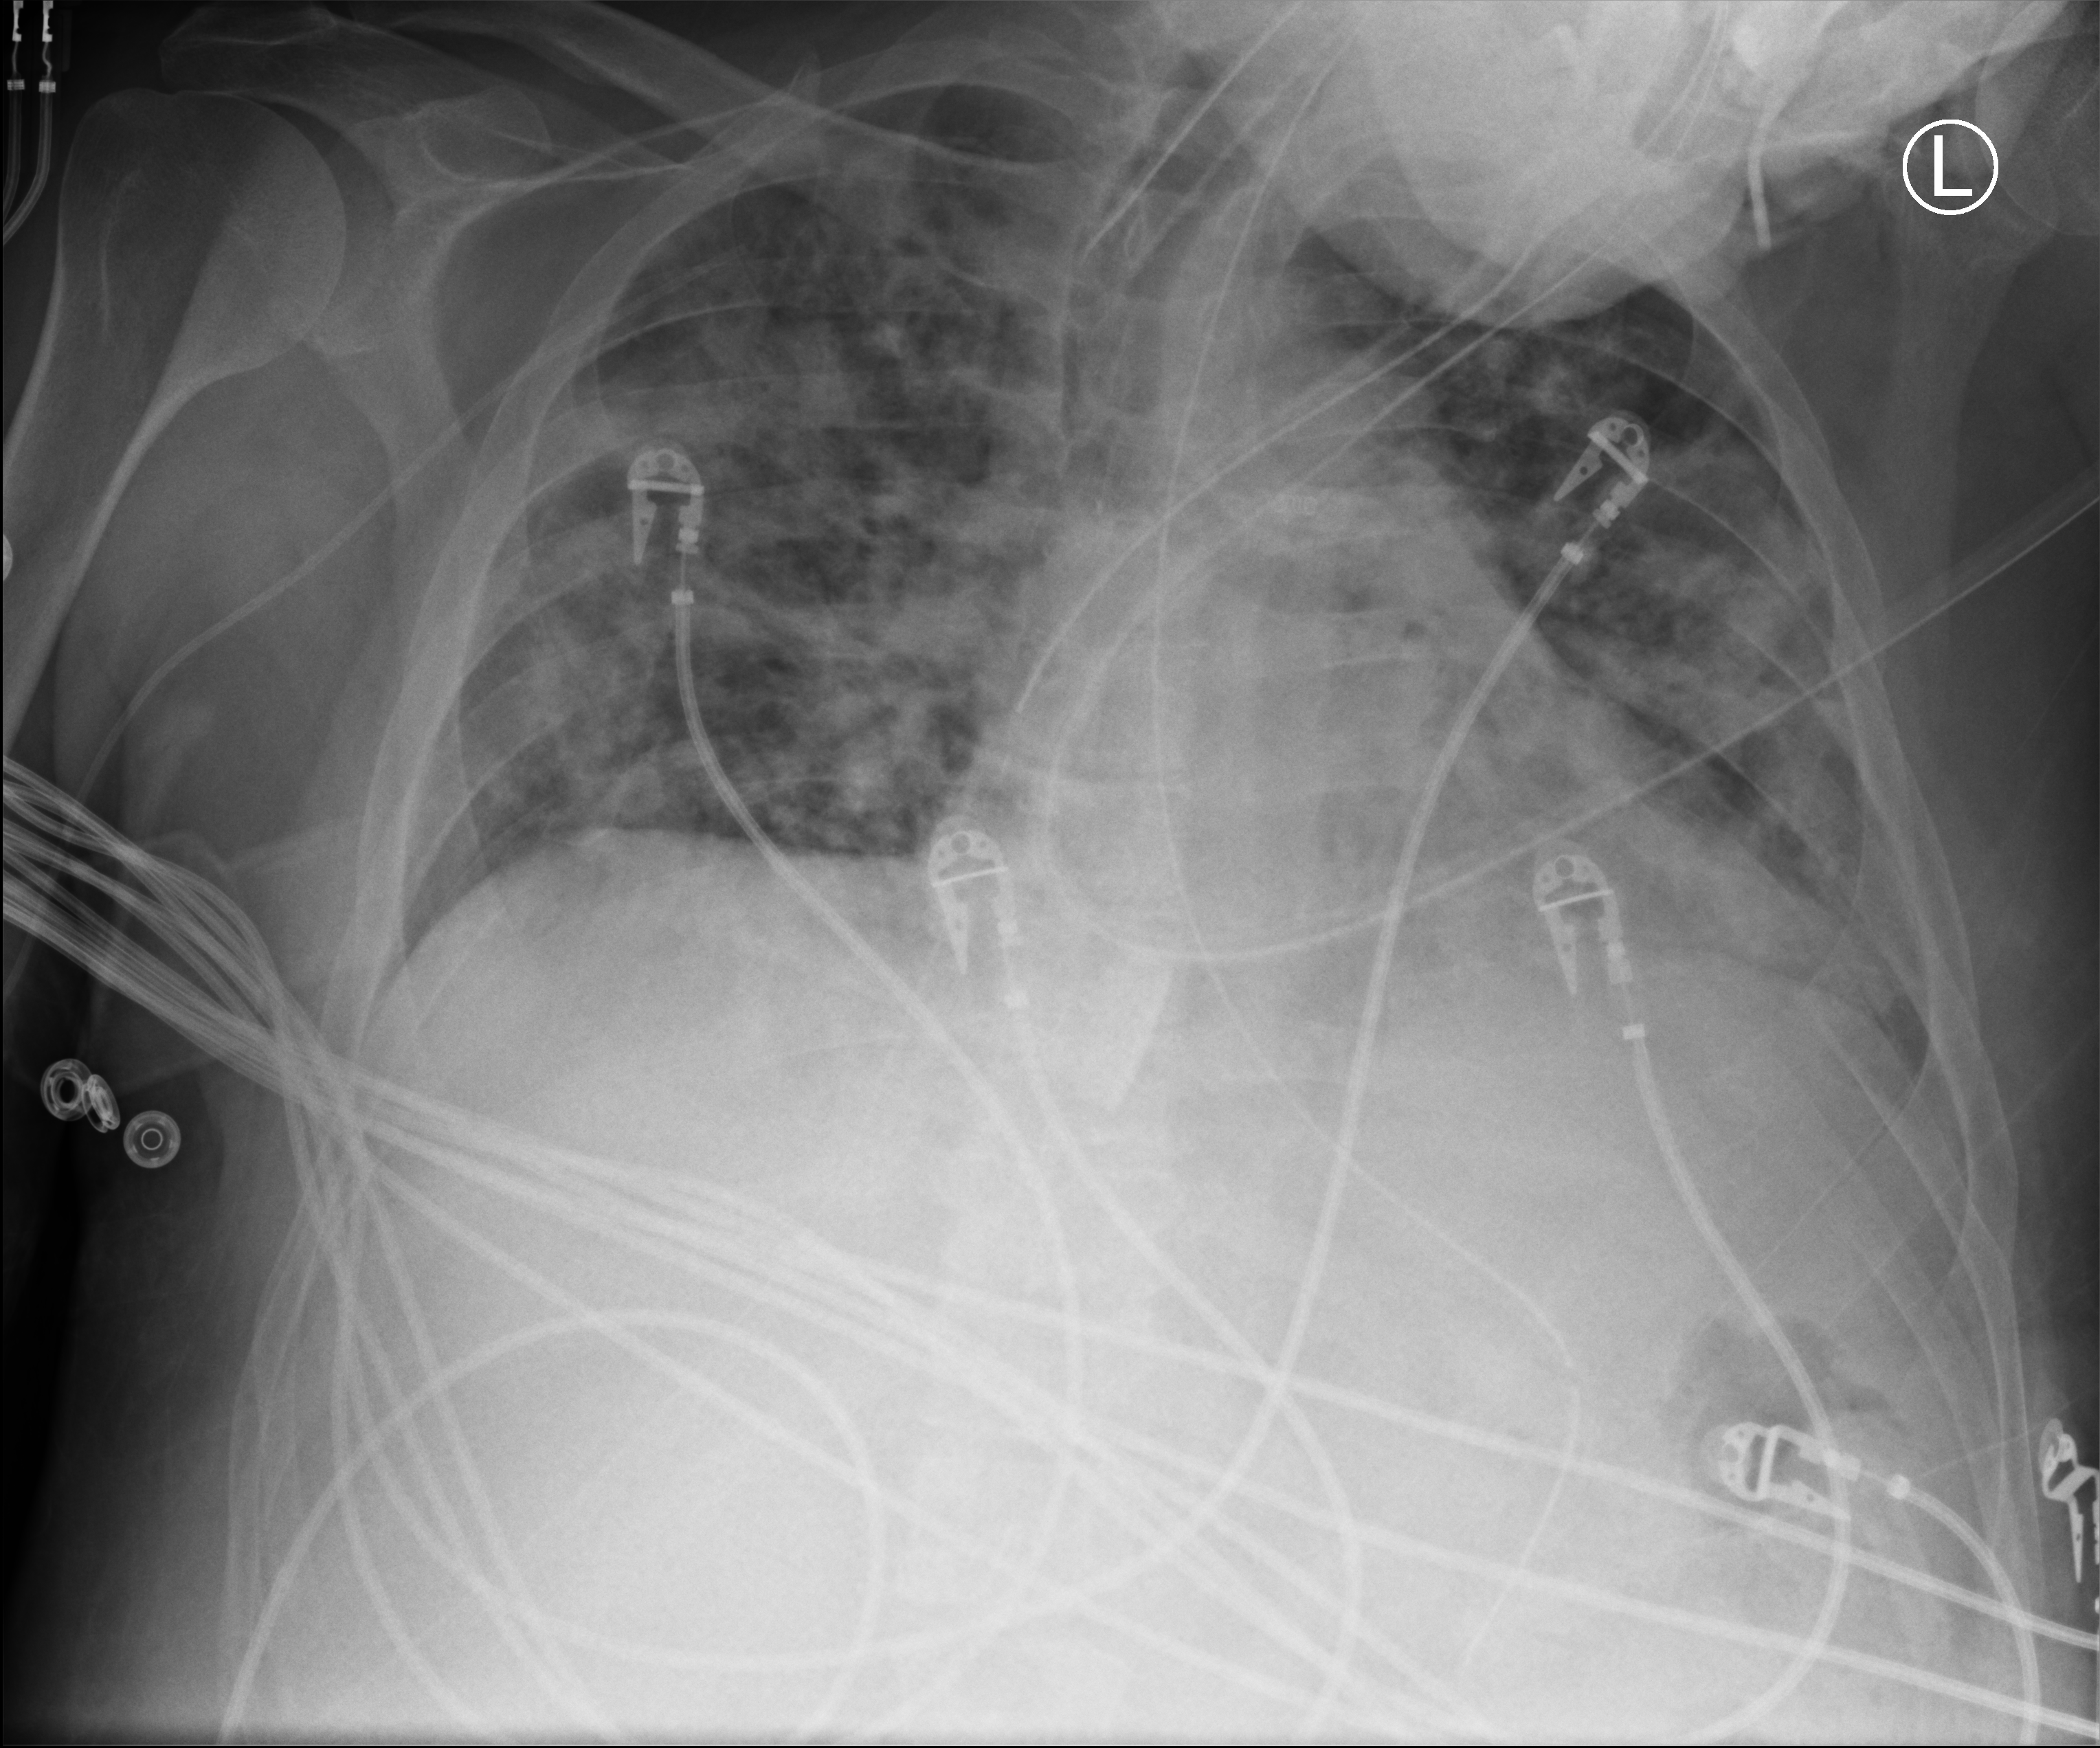
Chest X-ray (portable). Patient hospitalised with COVID-19; male, aged 18–59 years.
Admission-level facts for this patient (not findings on this image; timing relative to this image not recorded): admitted to intensive care during this hospital stay: yes; mechanically ventilated during this hospital stay: yes; hypertension (admission record): no.